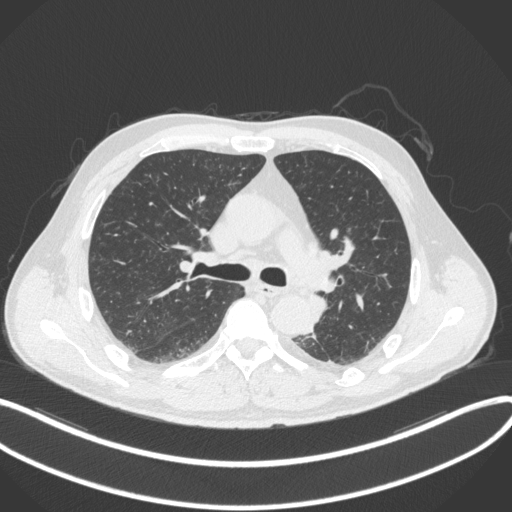
Chest CT, one axial slice. Reconstruction kernel B31f. Lung window (W 1500 / L -600 HU). 1 mm slice thickness. 512 × 512 image matrix, field of view 400 × 400 mm. Patient: male, 59 years. From the clinical record (not read from this slice): clinical TNM (as recorded): T2a N2 M0.
Outlined on this slice (rectangle marked by the reading radiologist):
- lung tumour (recorded histology: squamous cell carcinoma): bounding box [x1, y1, x2, y2] px = [306, 289, 330, 328]